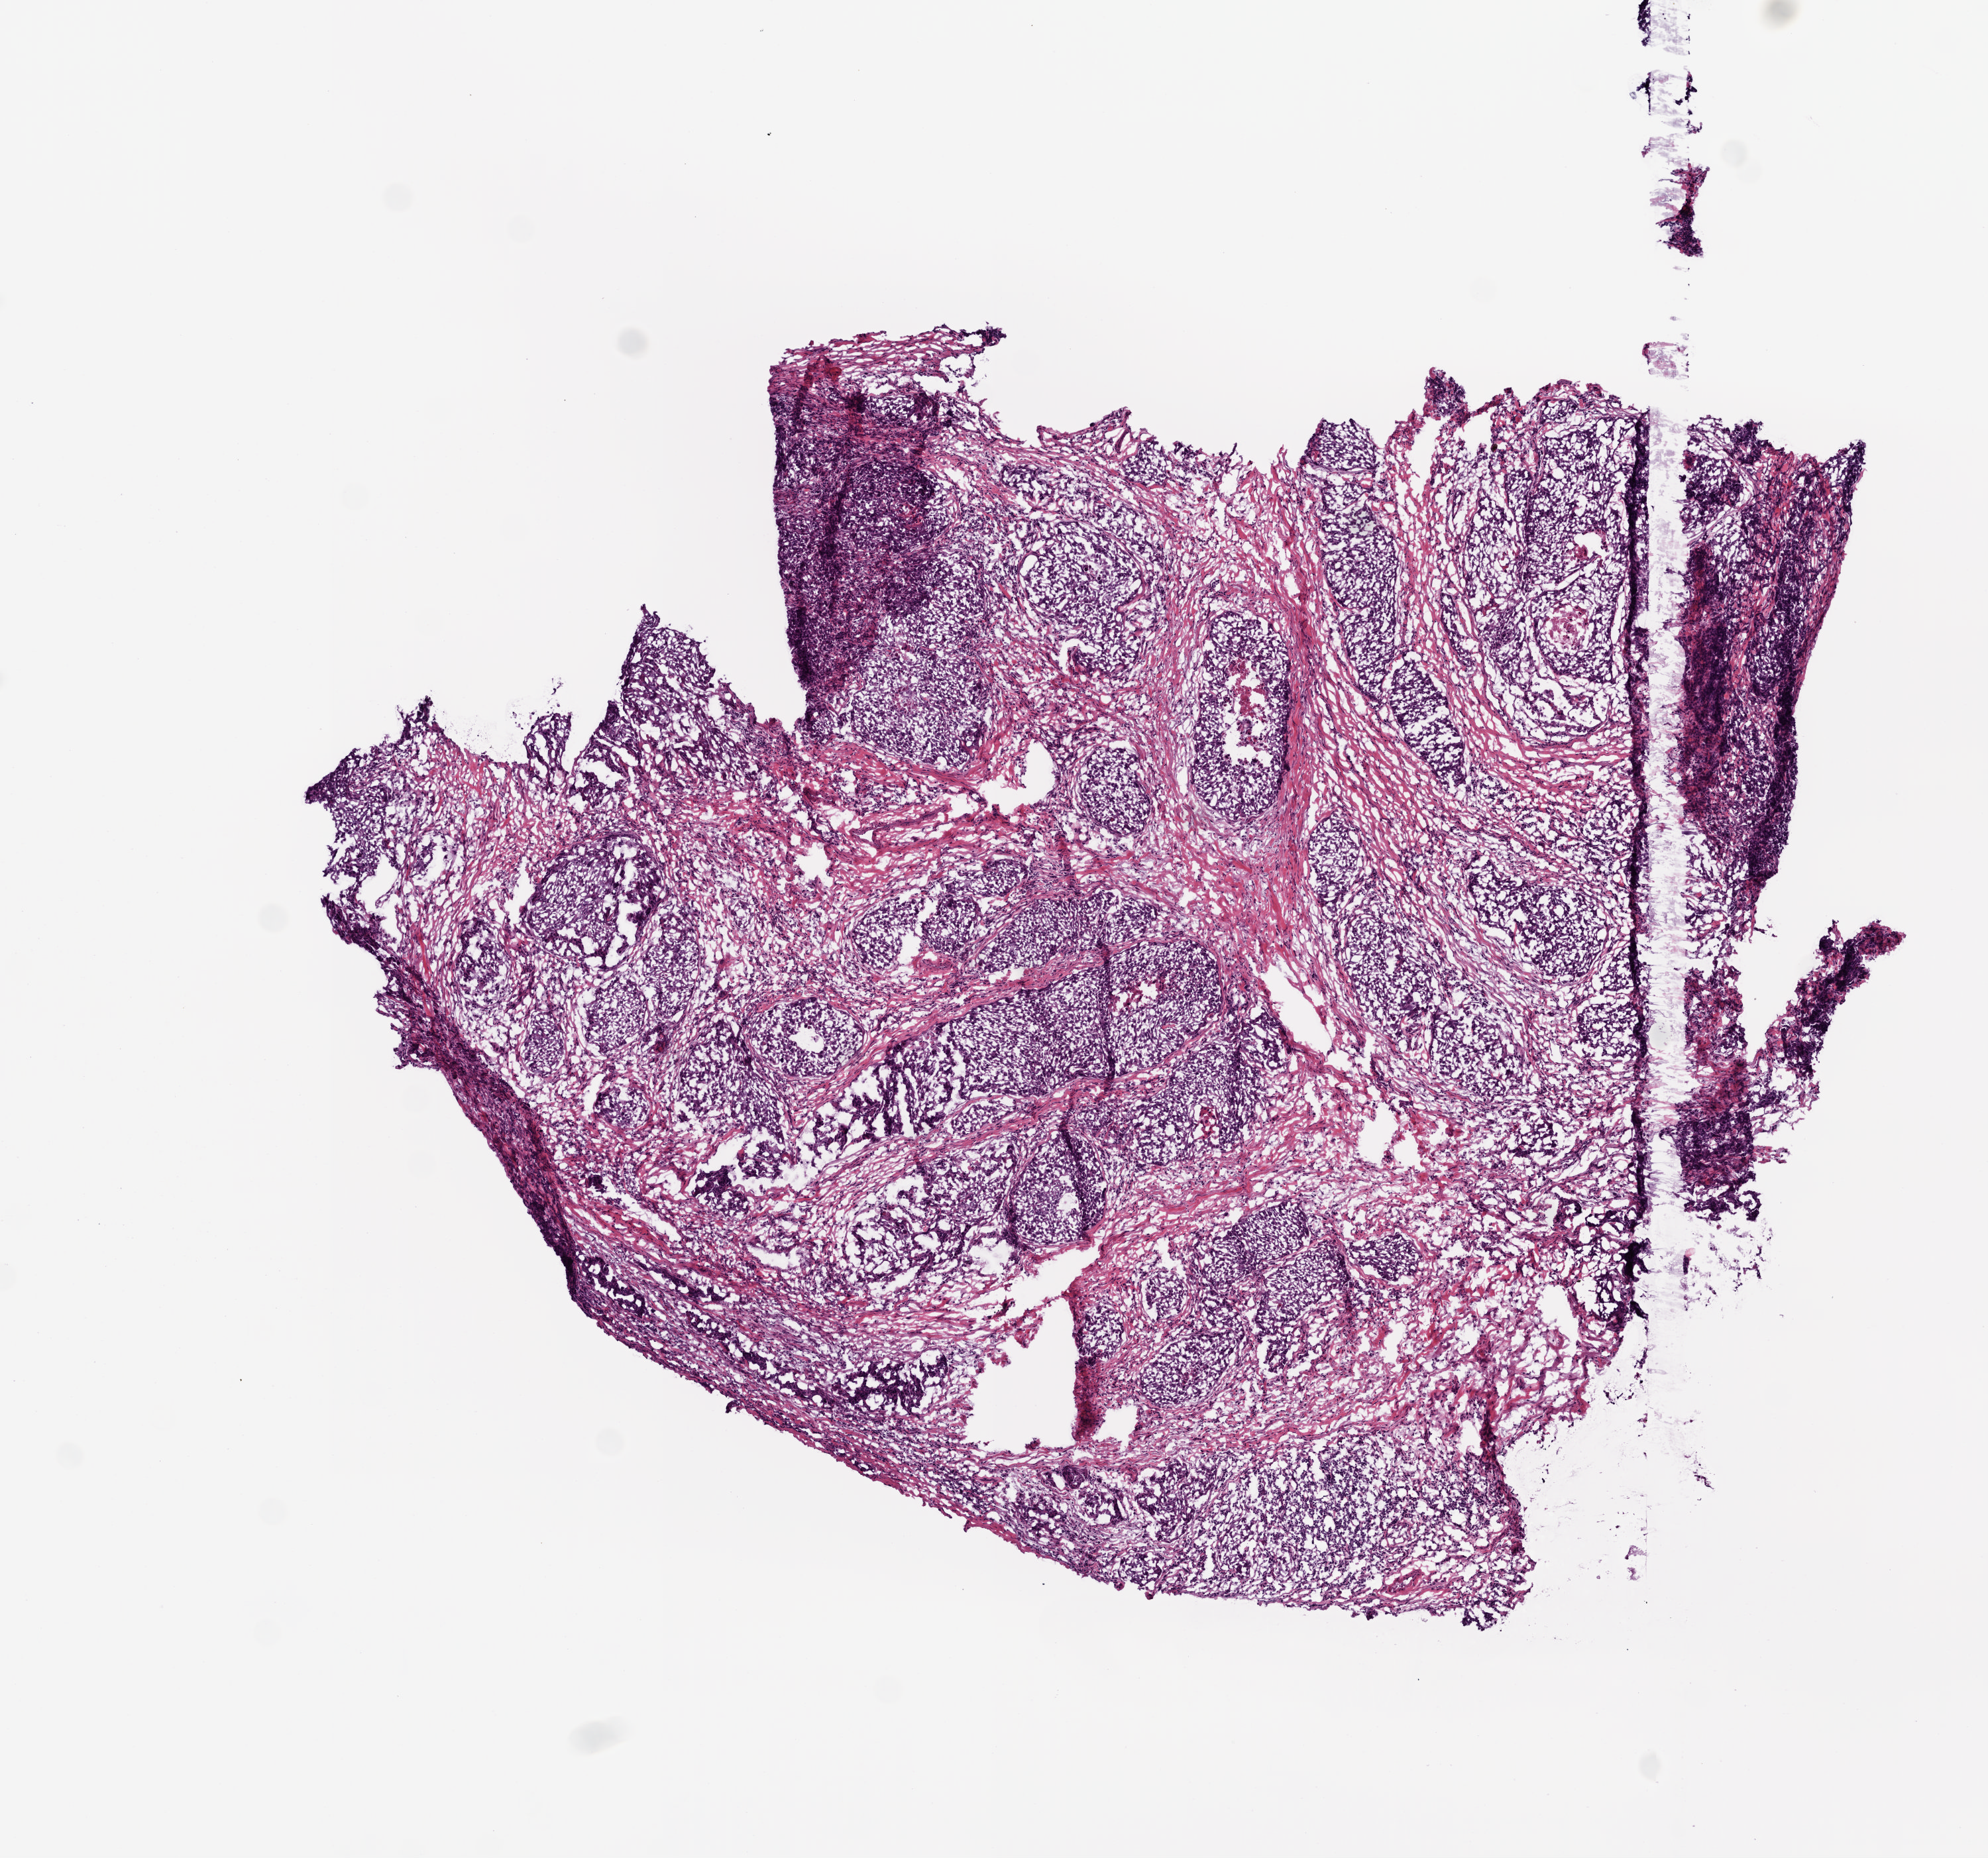
Whole-slide histology image, H&E-stained — low-resolution overview of the scanned area, about 6.0 x 5.6 mm (acquisition: 20x scan), frozen section from the bottom of the tissue portion, primary tumour sample from the head and neck. Male, age 61 years at initial diagnosis.
Diagnosis: Squamous cell carcinoma, NOS.